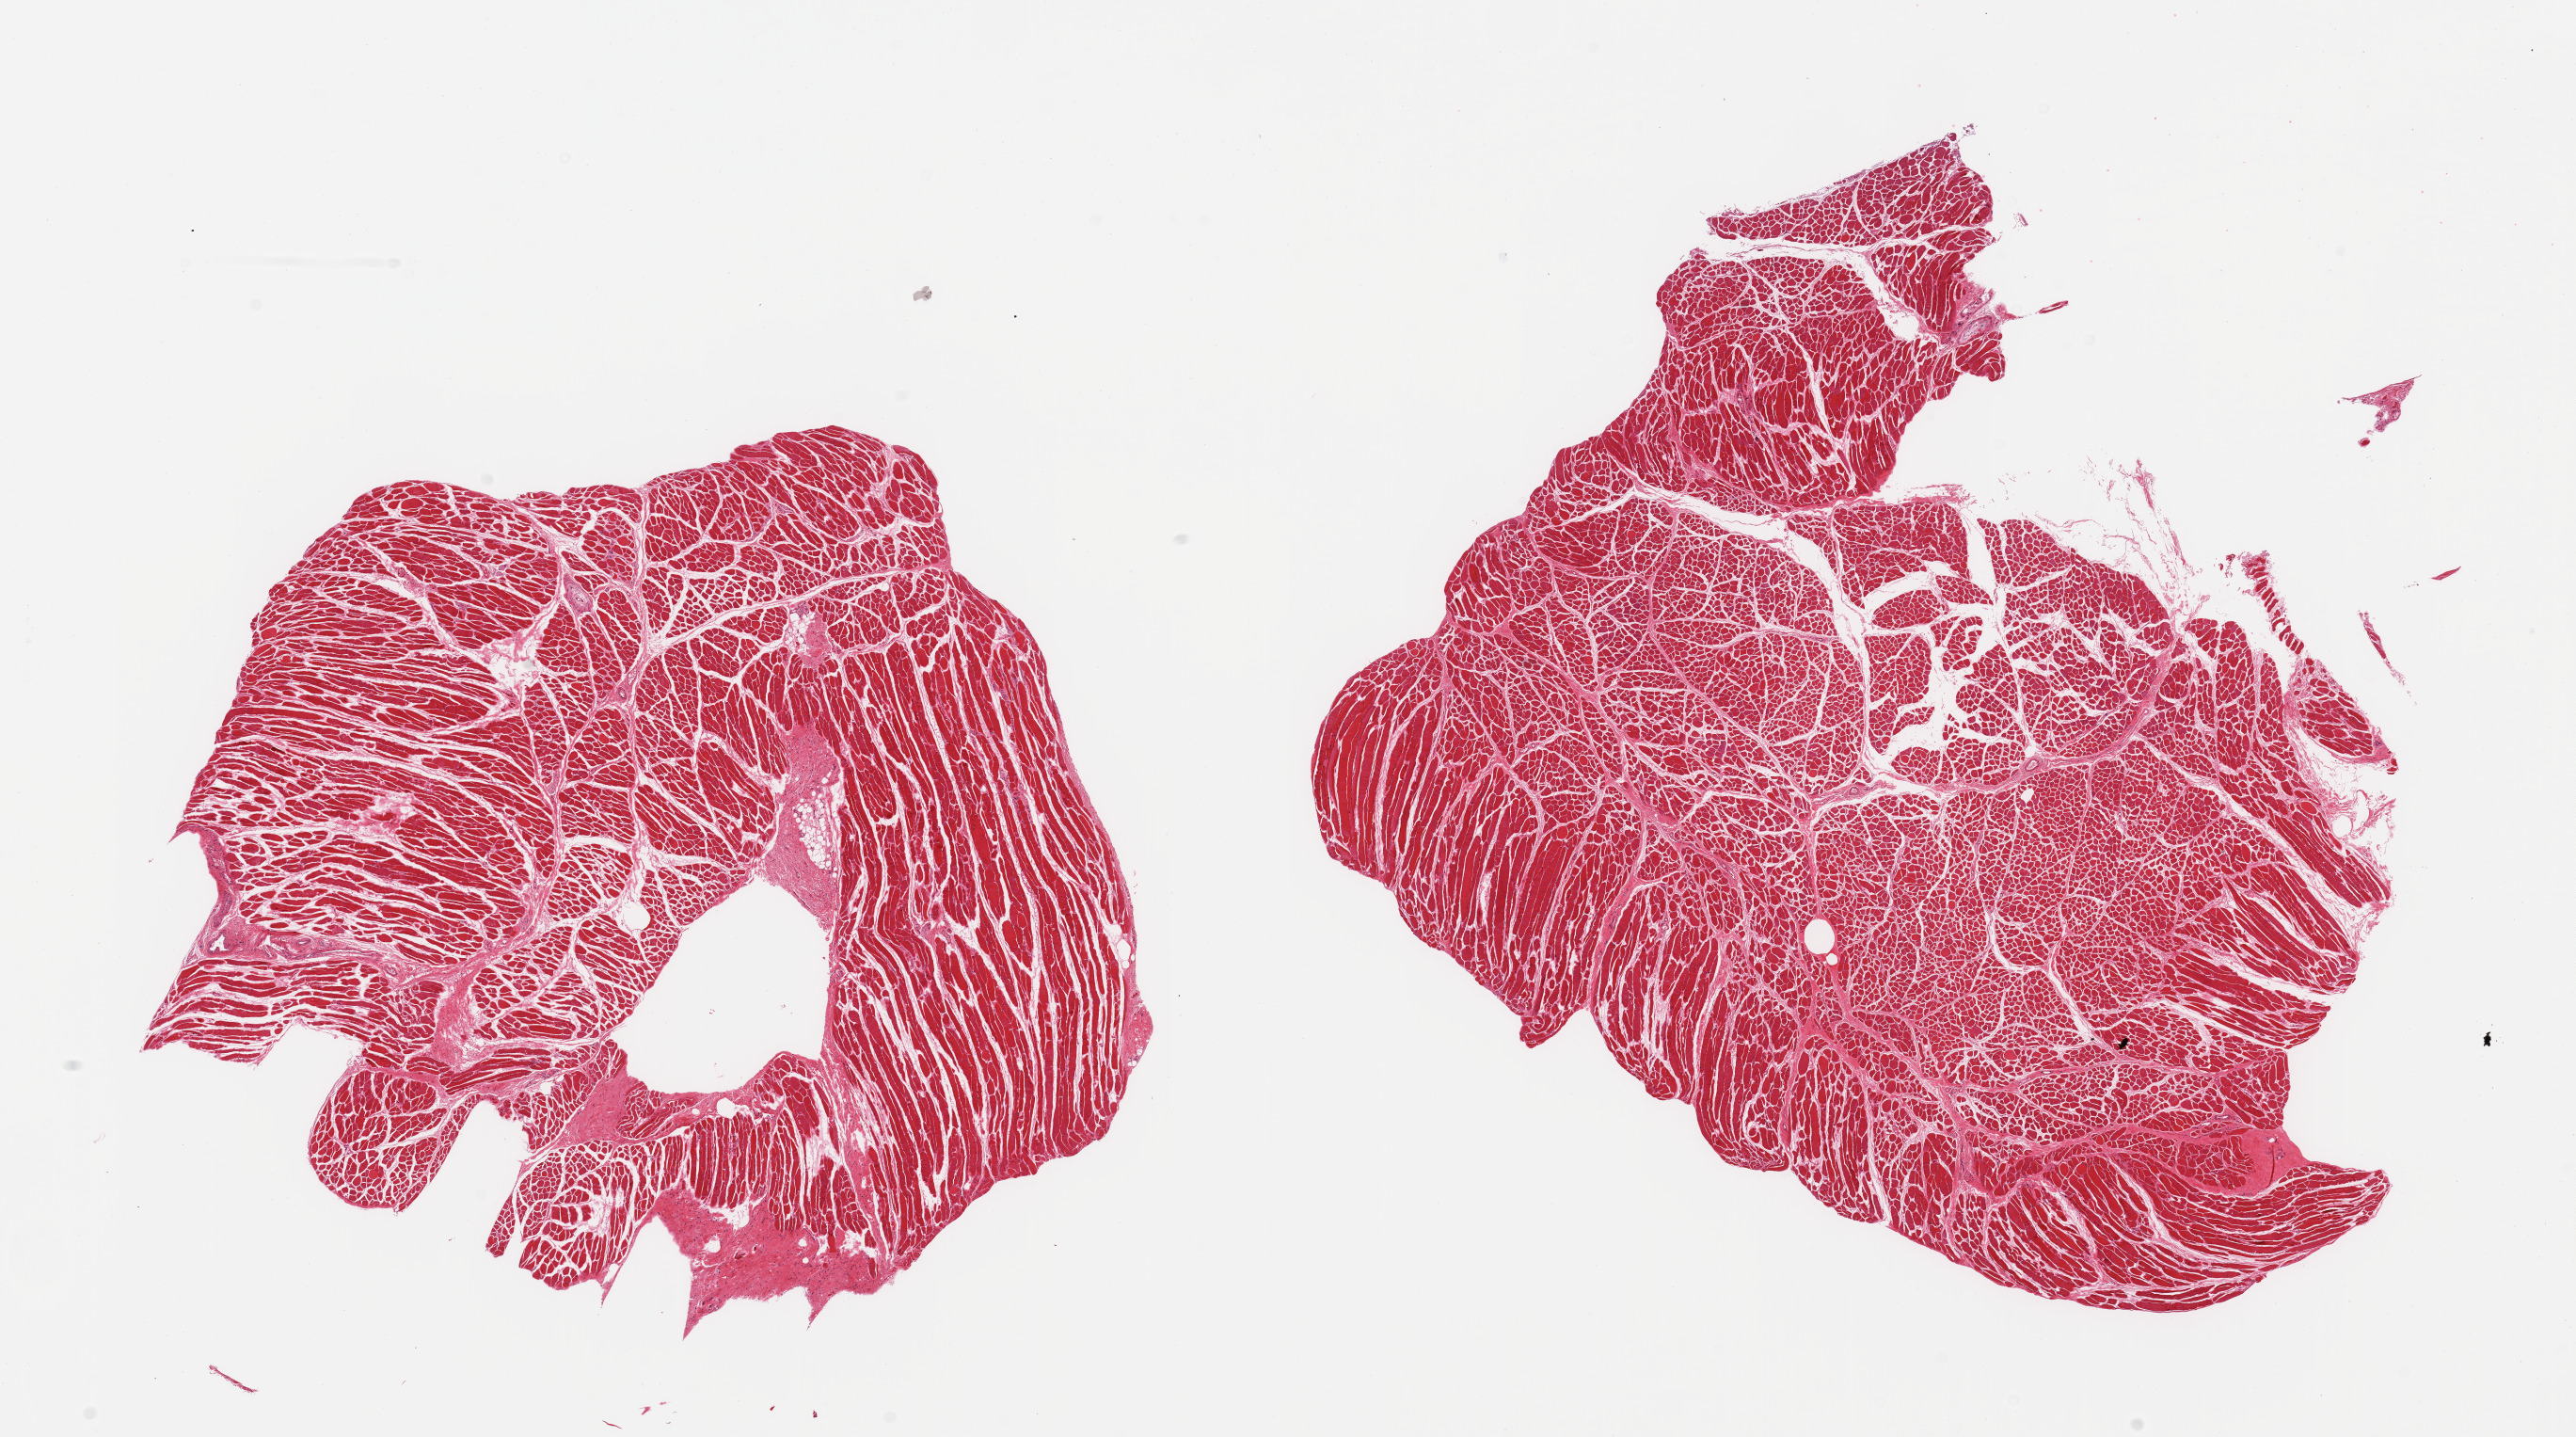
Haematoxylin and eosin whole-slide image, a low-resolution overview of the entire scanned area, about 21.7 x 12.1 mm (acquisition: 20x scan); PAXgene-fixed paraffin-embedded (PFPE) section; target tissue: thyroid; donor tissue sample.
Review note (as recorded): 2 pieces; not thyroid, skeletal muscle.